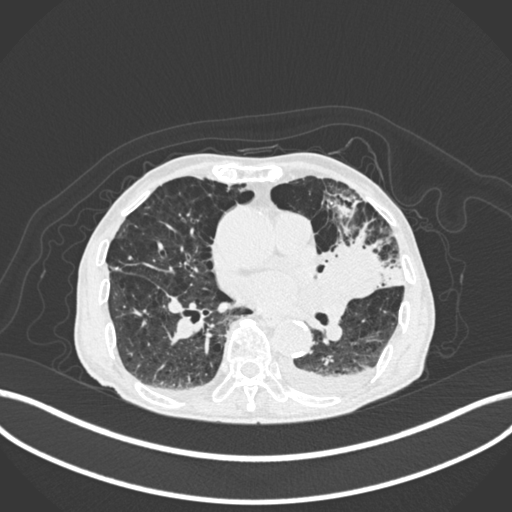
Chest CT, one axial slice; position 100 of 400 along the scan axis; reconstruction kernel B30f; lung window (W 1500 / L -600 HU); 512 × 512 image matrix. Male patient, age 90 years or older. From the clinical record (not read from this slice): clinical TNM (as recorded): T2b N1 M0.
Structures marked on this image (bounding box drawn by a radiologist):
- lung tumour (recorded histology: squamous cell carcinoma): box from (x=319, y=233) to (x=384, y=299) px